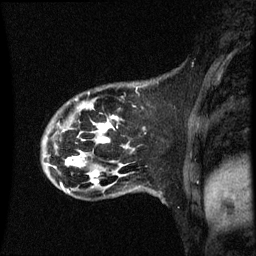
Breast MRI (dynamic contrast-enhanced), one sagittal slice. Position 15 of 60 along the scan axis. Dynamic contrast-enhanced series, image 2 of 3 at this slice position (ordered by acquisition). 1.5 T. TE 4.2 ms, TR 8.9 ms. 2 mm slice thickness. 256 × 256 image matrix, field of view 200 × 200 mm. Patient: female, 44 years. From the clinical record (not read from this slice): setting: breast cancer imaged before/during neoadjuvant chemotherapy; receptor status: HR-positive, HER2-negative.
Outlined on this slice (semi-automatically segmented with operator editing):
- analysis volume of interest (the breast-tissue region the enhancement analysis was run in; not a lesion): bounding box (x1, y1, x2, y2) in pixels: (43, 84, 144, 189)
- tumour enhancement mask (voxels above the 70 % enhancement threshold inside the analysis volume of interest): (65, 116, 117, 183)